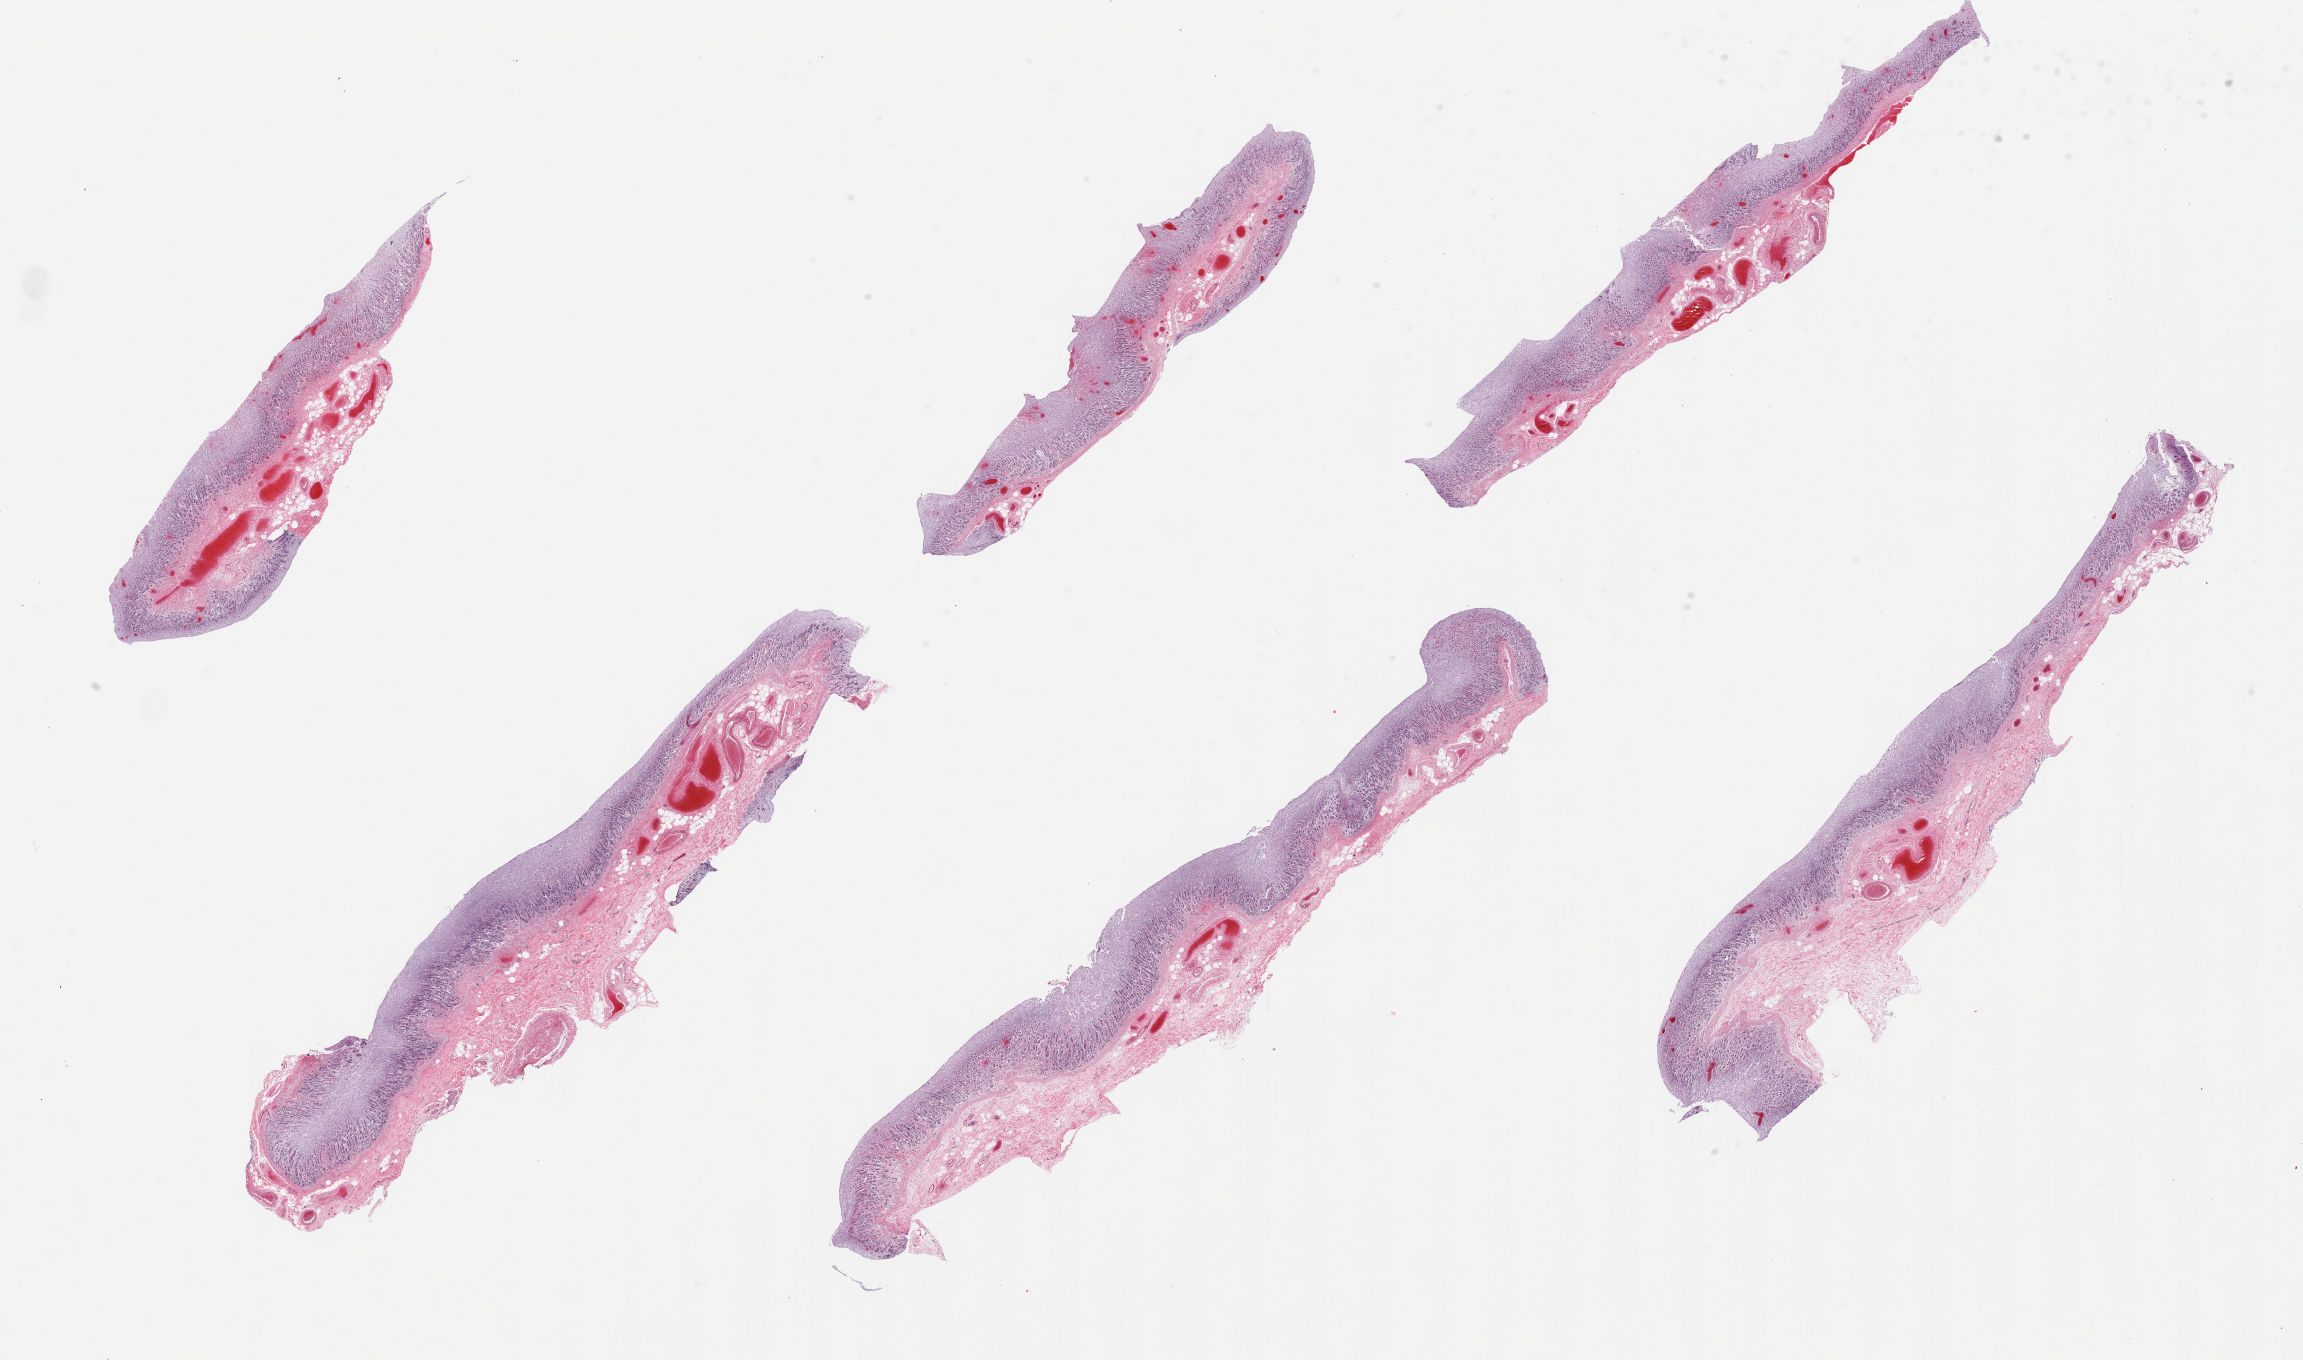
H&E whole-slide image, a low-resolution overview of the entire scanned area, about 36.4 x 21.5 mm (acquisition: 20x scan); PAXgene-fixed, paraffin-embedded tissue; sampled site (target tissue): stomach; donor tissue sample. Male donor.
* pathologist's review note for this sample: 6 pieces, 70-80% muscosa, but completely autolyzed